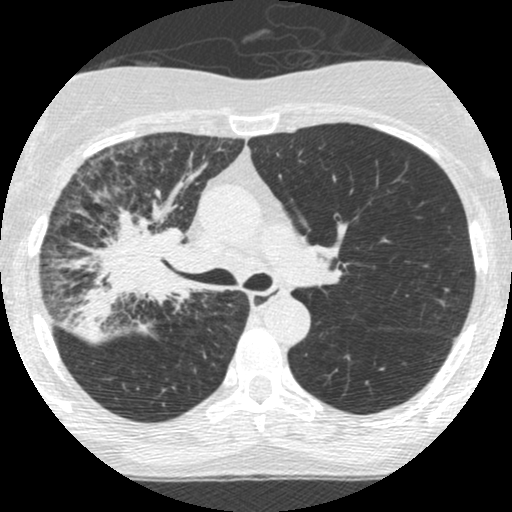
Low-dose screening chest CT, one axial slice. Slice 167 of 253 in the series (ordered by position). Lung window (W 1500 / L -600 HU). 1.25 mm slice thickness. 512 × 512 image matrix, field of view 294 × 294 mm.
Structures marked on this image (manually delineated by an expert):
- lesion 2 (tumor, hilum of right lung): box from (x=69, y=195) to (x=189, y=328) px